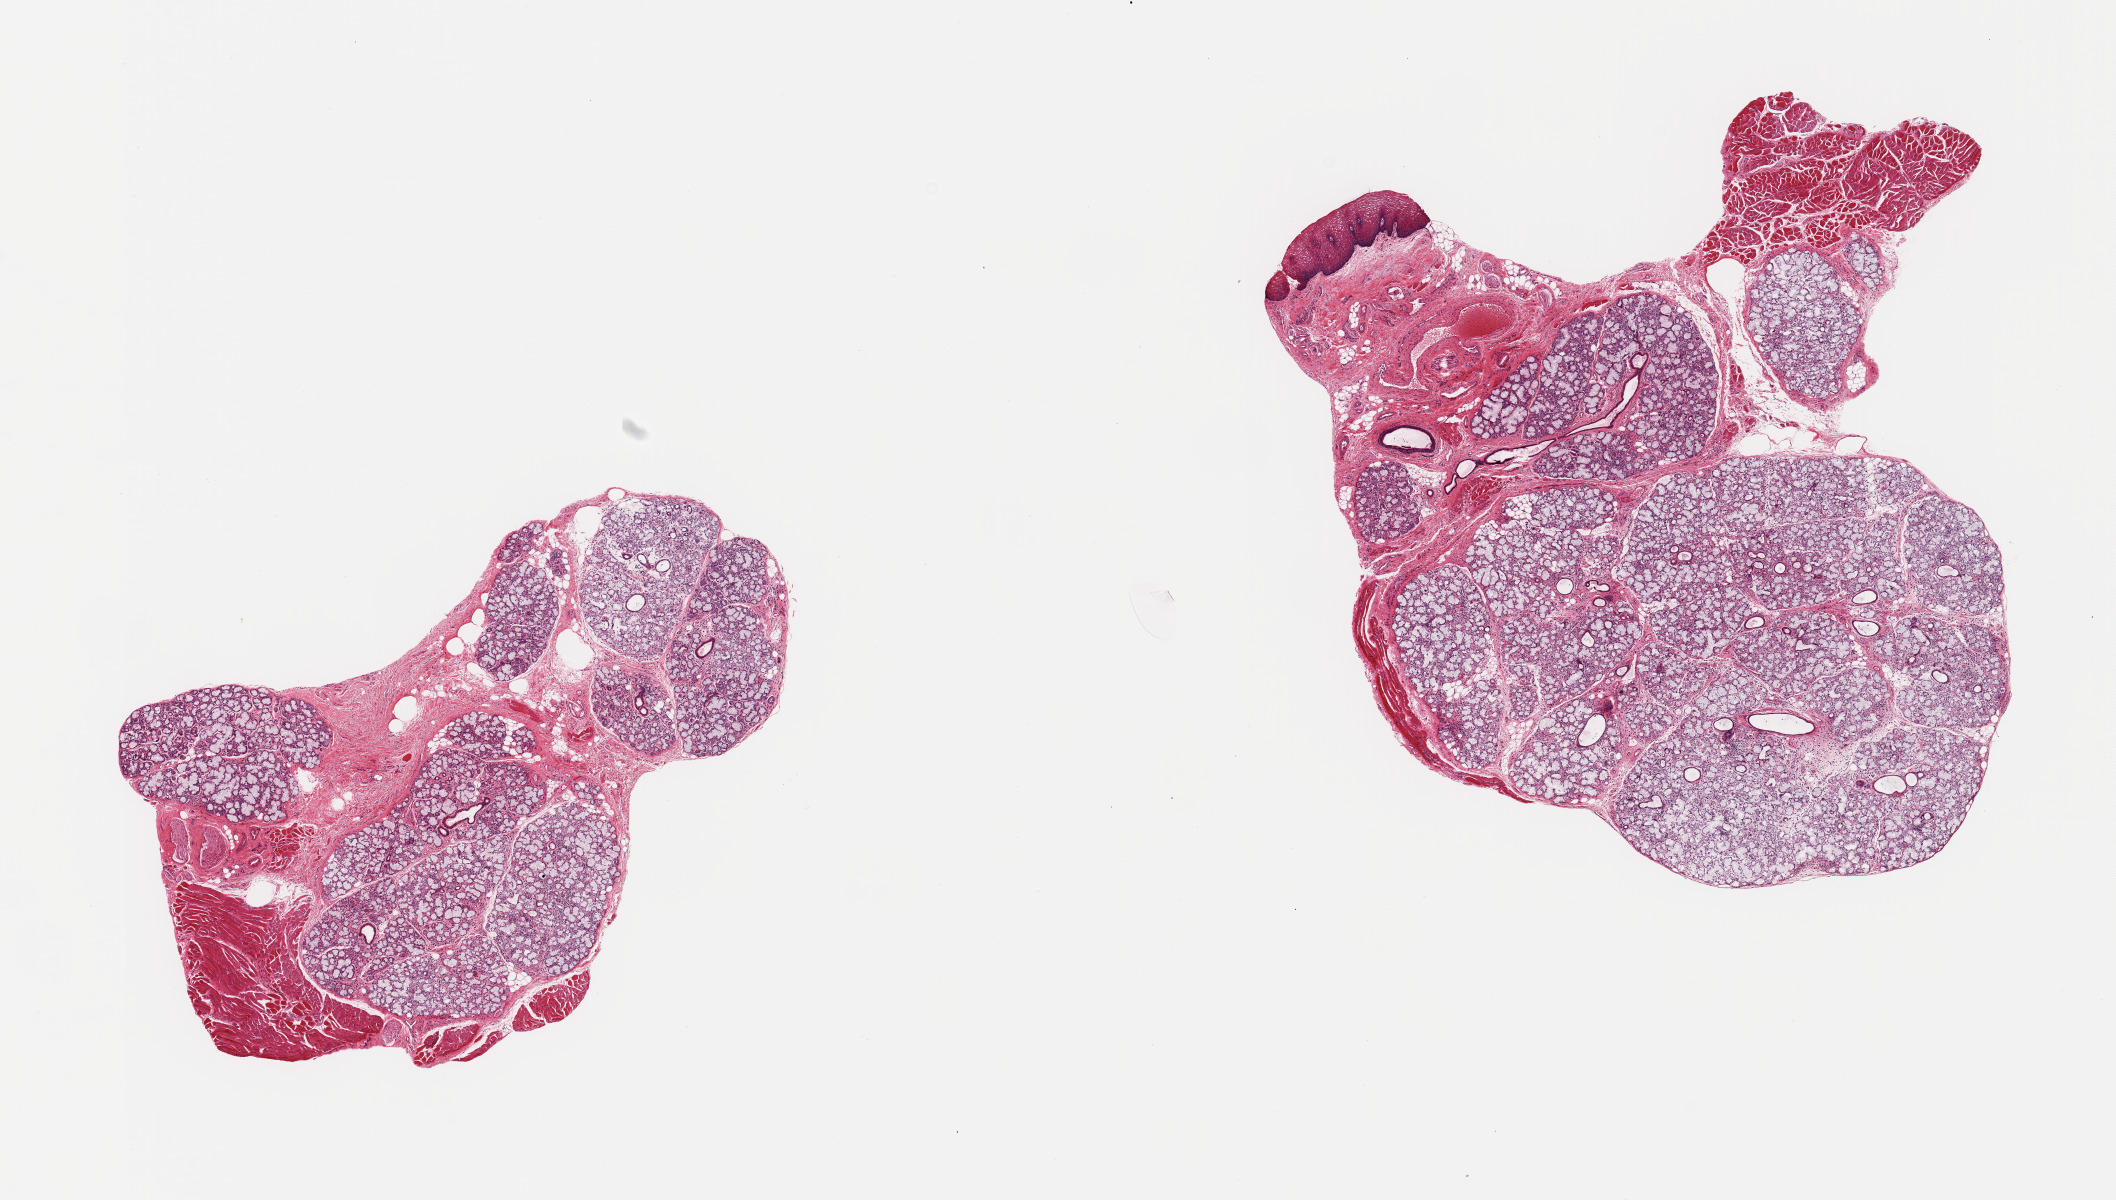
Digitized H&E-stained section — a low-resolution overview of the entire scanned area, about 16.7 x 9.5 mm (from a 20x scan), PAXgene-fixed, paraffin-embedded tissue, target tissue: minor salivary gland, tissue donor sample.
* pathologist's review note for this sample: 2 pieces; attached ~15% skeletal muscle and one piece with attached squamous mucosa and submucosa